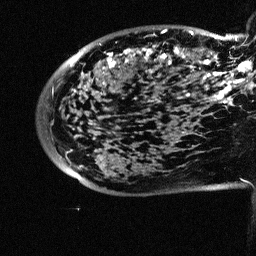
Breast MRI (dynamic contrast-enhanced), one sagittal slice; position 15 of 64 along the scan axis; dynamic contrast-enhanced study with each time point stored as its own series, time point 2 of 3 at this slice position (early post-contrast, ordered by acquisition time); 1.5 T; TE 4.5 ms, TR 11 ms; 2.5 mm slice thickness; 256 × 256 image matrix, field of view 200 × 200 mm. Female patient, age 38 years. Case-level facts recorded for this patient, not image findings: setting: breast cancer imaged before/during neoadjuvant chemotherapy; receptor status: HR-positive, HER2-negative.
Structures marked on this image (semi-automatic segmentation, software-assisted and operator-edited):
- analysis volume of interest (the breast-tissue region the enhancement analysis was run in; not a lesion): box from (x=88, y=18) to (x=252, y=126) px
- tumour enhancement mask (voxels above the 90 % enhancement threshold inside the analysis volume of interest): (x=108, y=30)–(x=252, y=107)